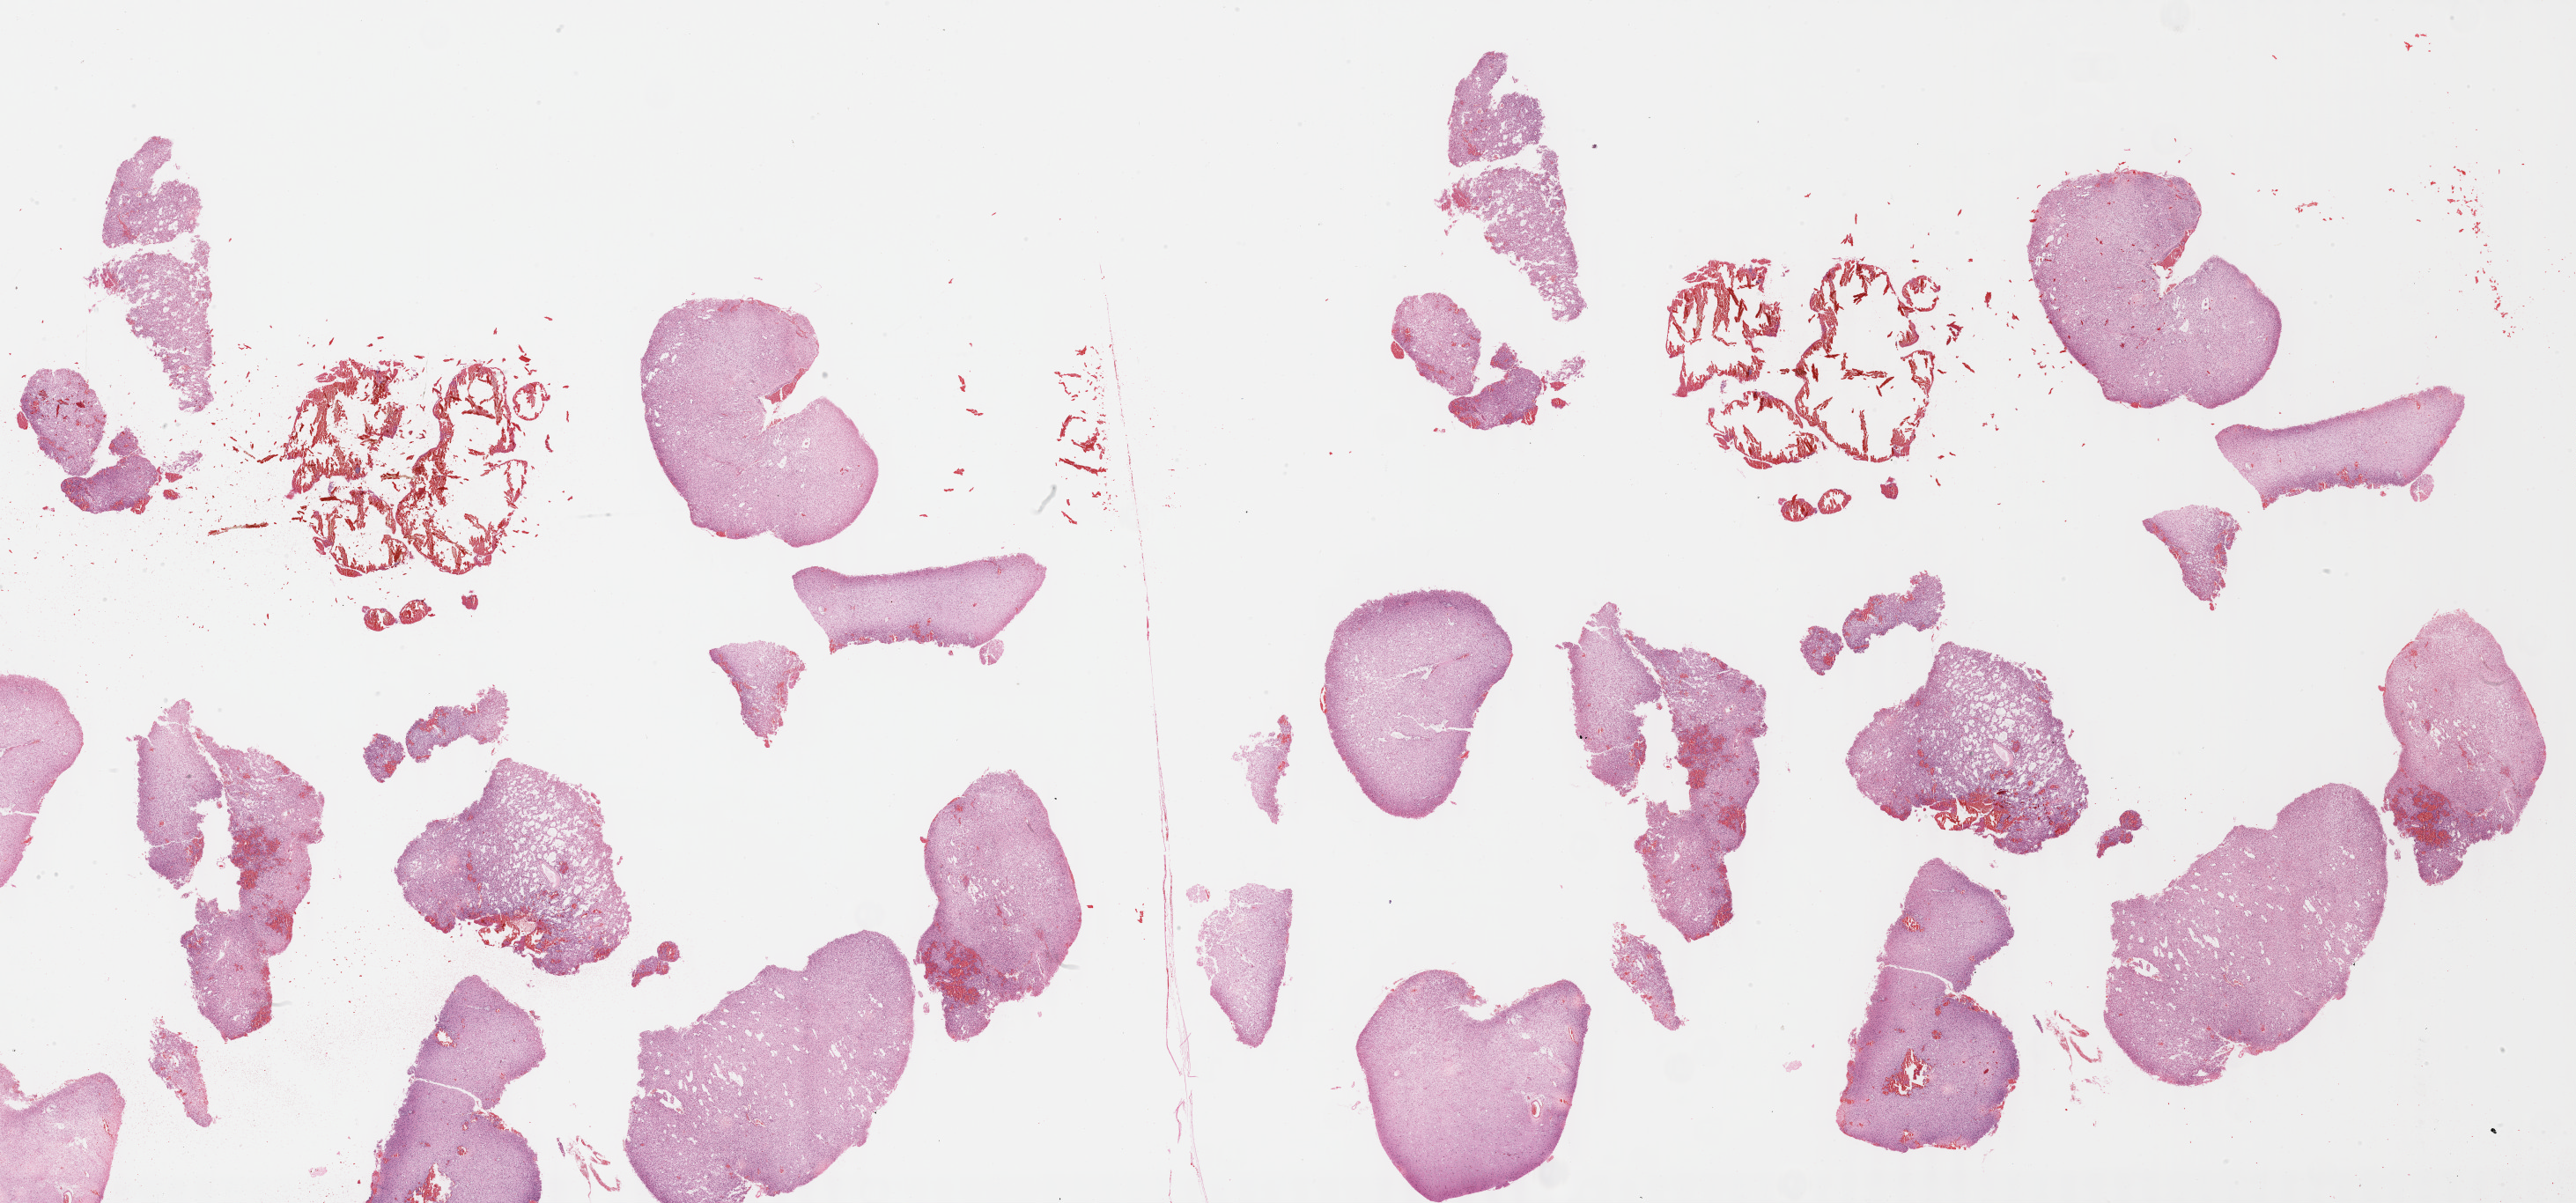
H&E-stained whole-slide image, shown as a low-resolution overview of the whole scanned area (about 47.3 x 22.1 mm, acquisition: 40x scan); FFPE section; primary tumour sample from the brain. Female patient; age at initial diagnosis 42 years. Histologic grade: G2 (moderately differentiated).
* pathologic diagnosis: Oligodendroglioma, NOS (cerebrum)
* laterality: left